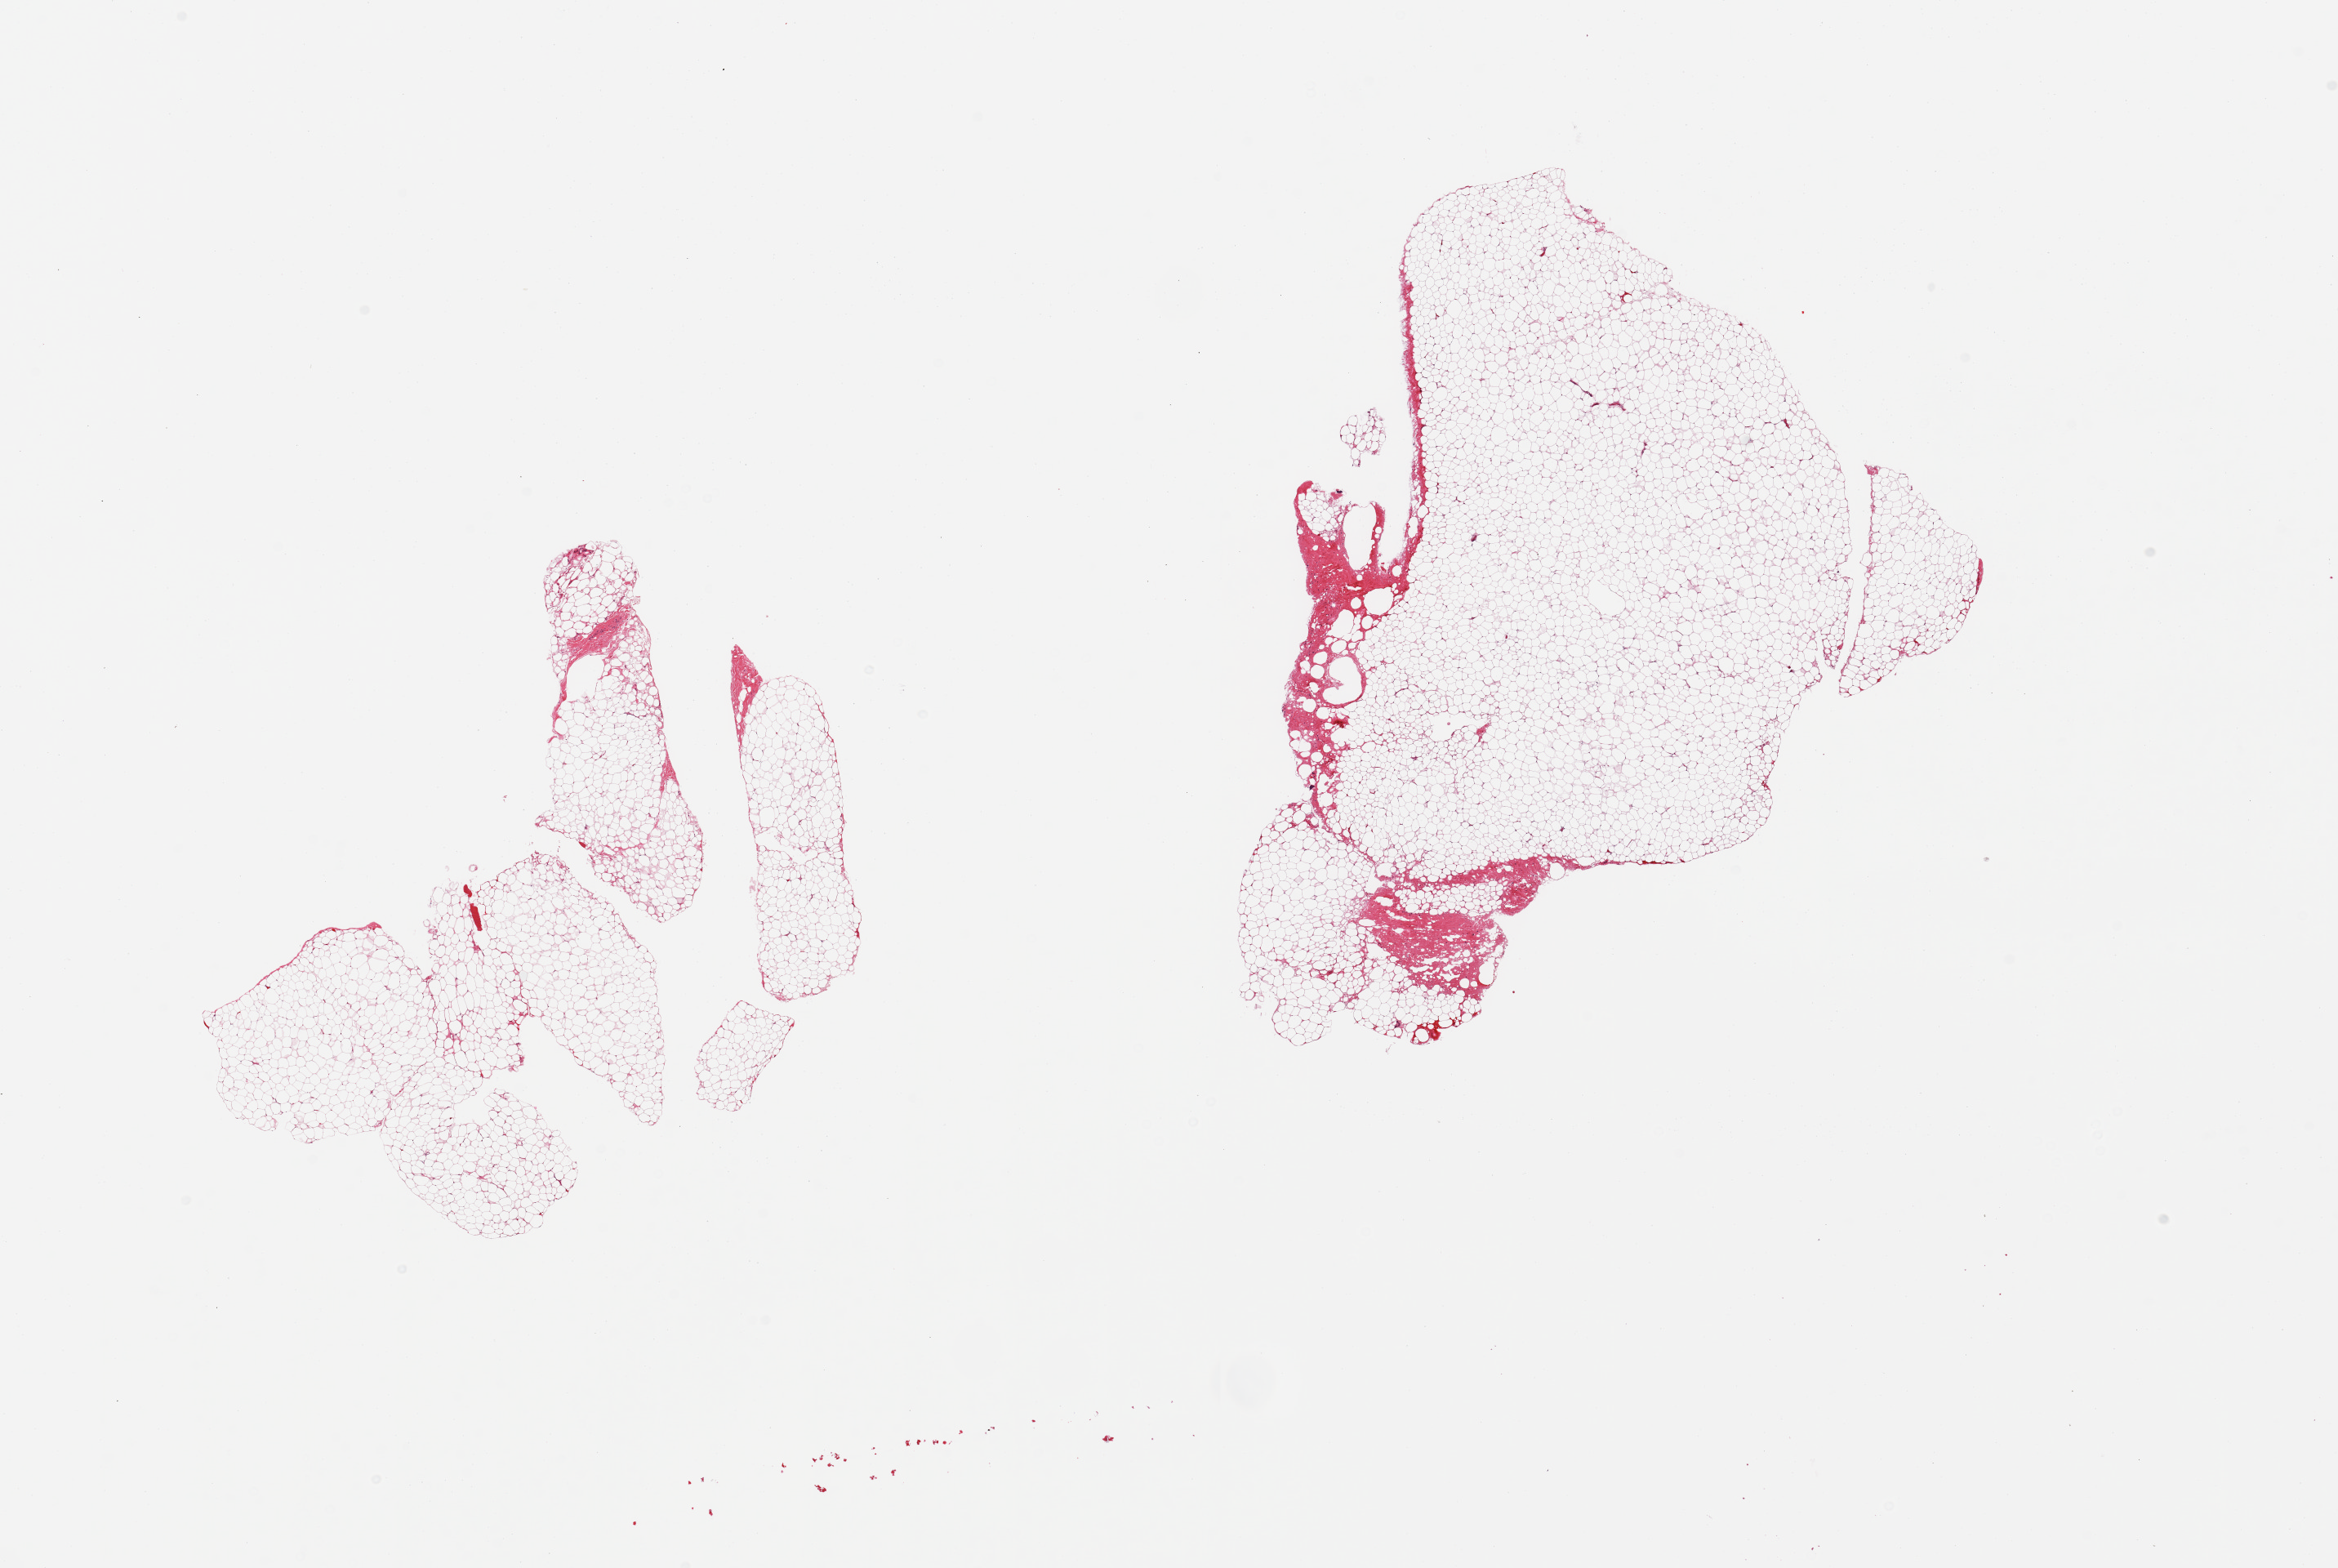
Digitized haematoxylin and eosin-stained section — low-resolution overview of the scanned area, about 22.6 x 15.2 mm (slide scanned at 20x); PAXgene-fixed paraffin-embedded (PFPE) section; target tissue: breast; tissue donor sample. Male donor.
• pathologist's review note for this sample: 2 pieces; adipose tissue with 5% fibrous content; no mammary ducts